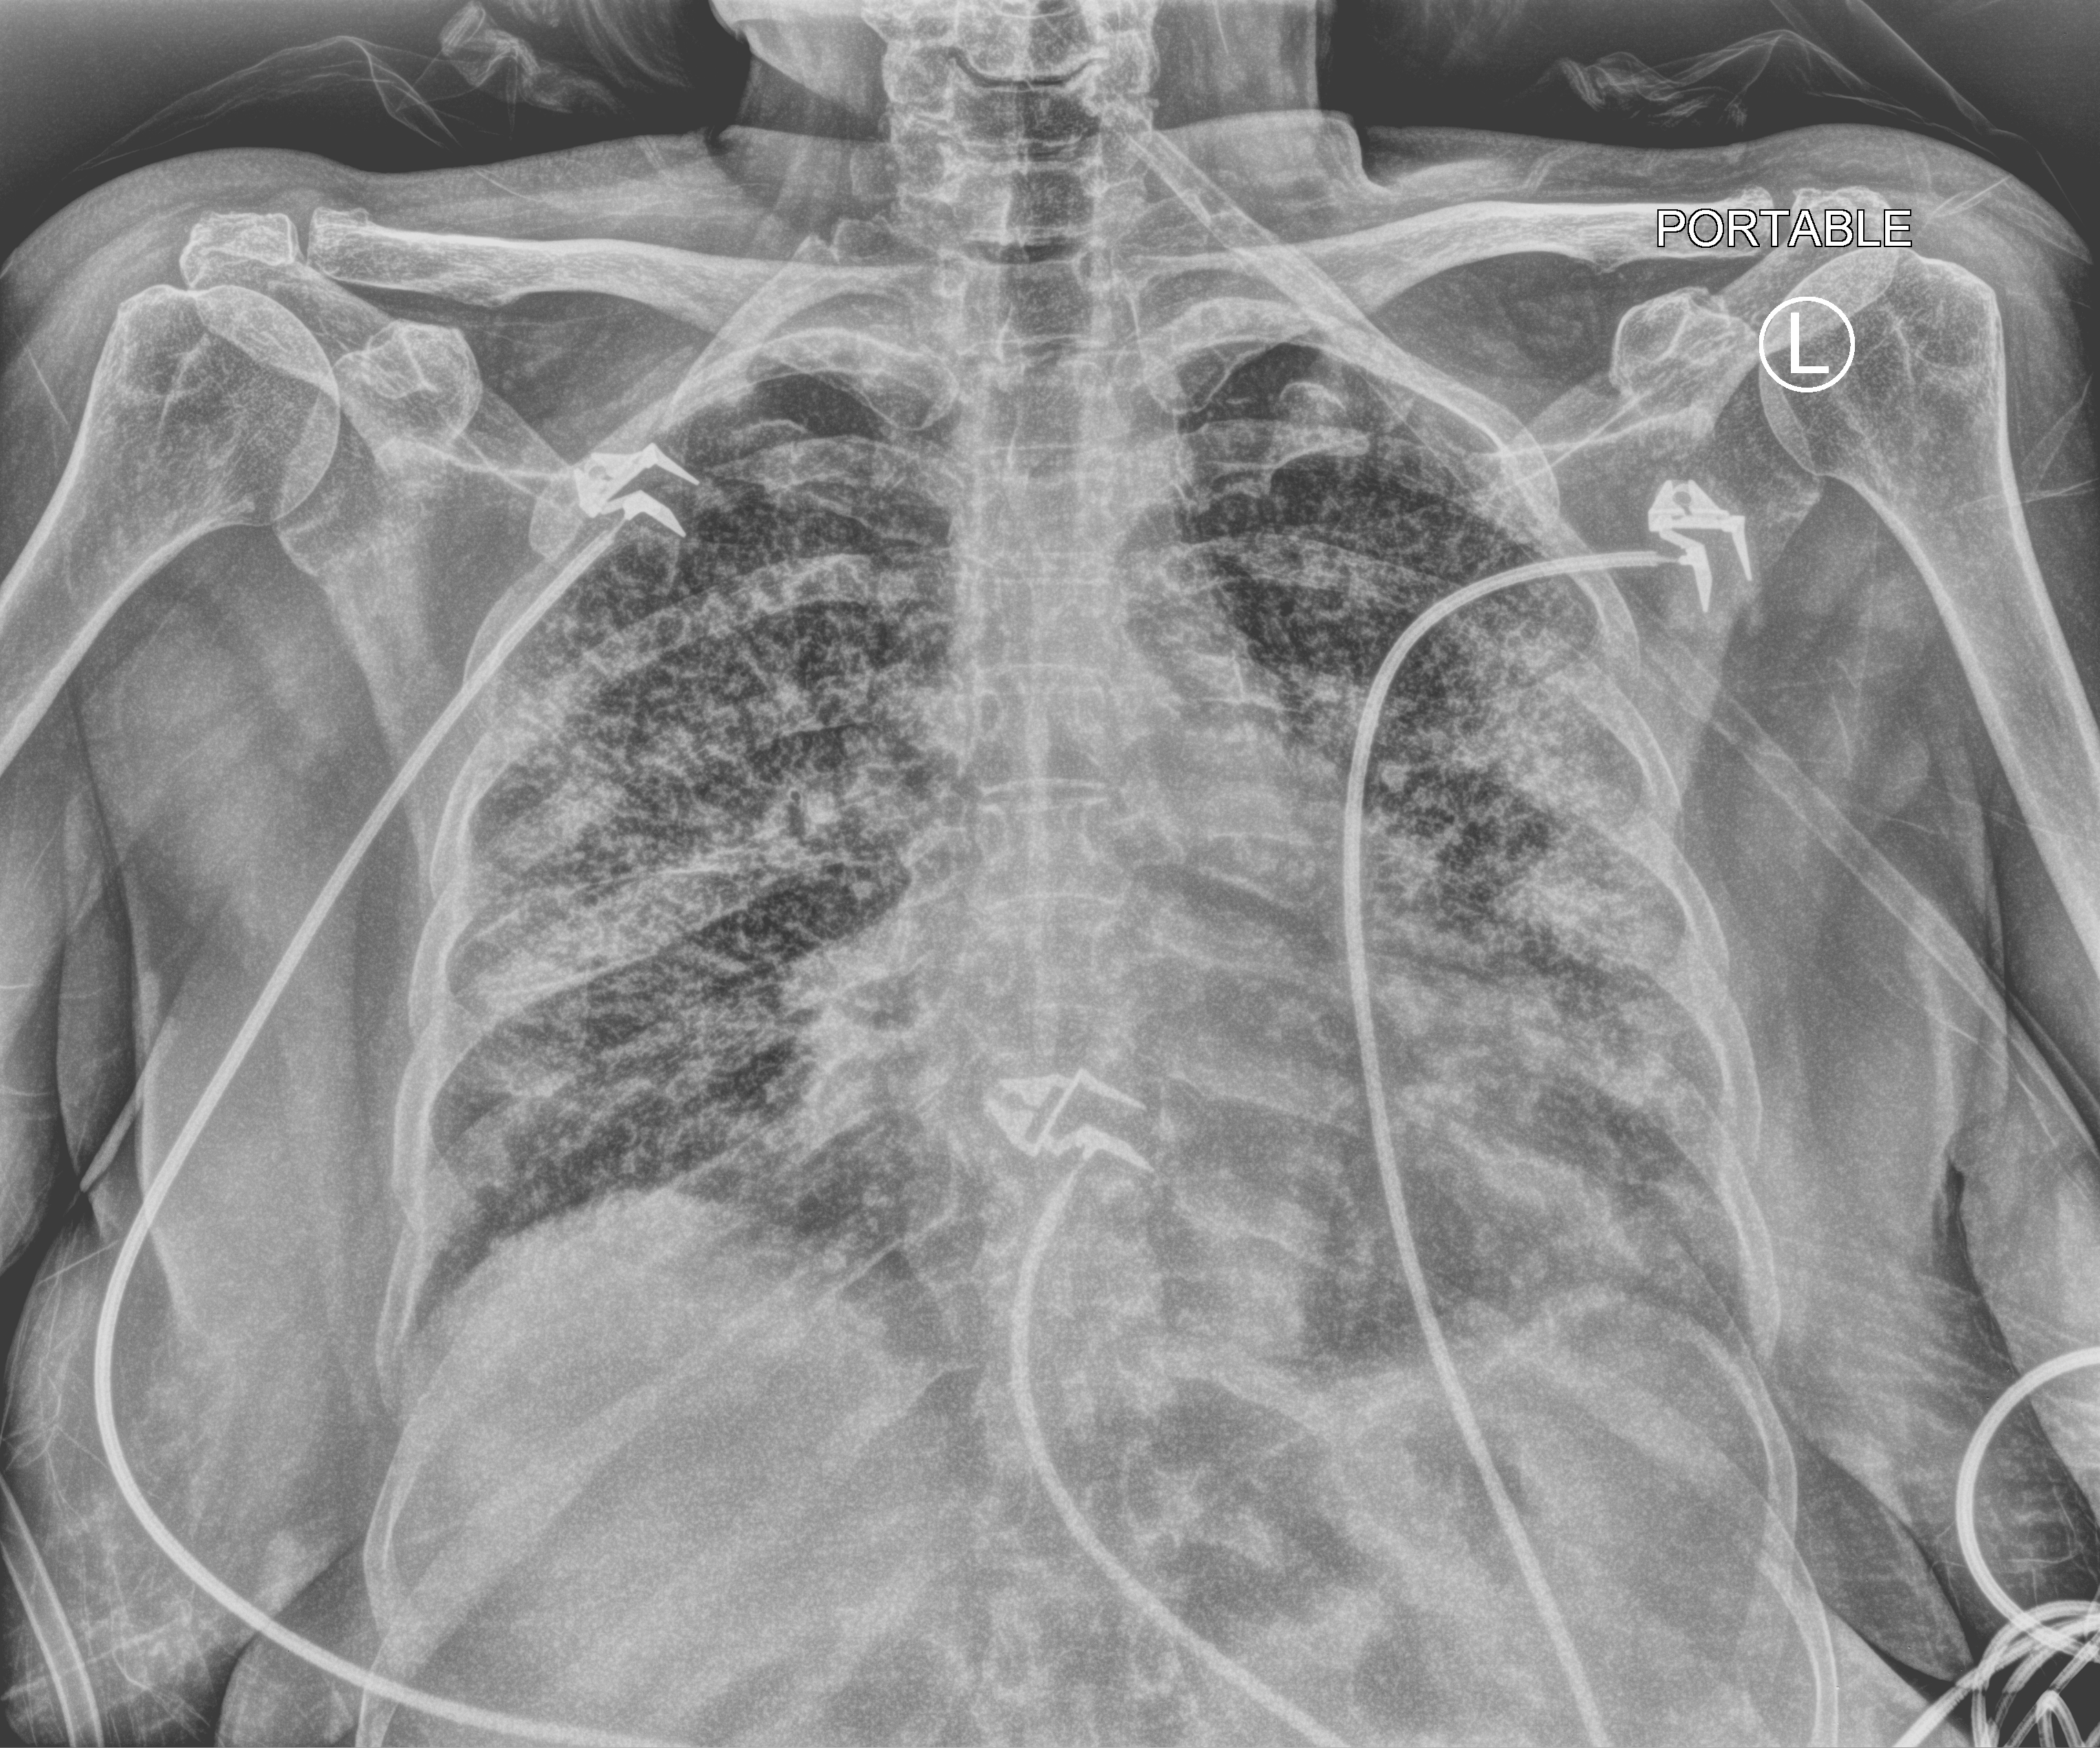
Bedside chest radiograph (computed radiography), anteroposterior (AP) projection. Female patient hospitalised with COVID-19, age 60–74 years.
From the hospital-stay record, not from the radiograph (when in the stay this image was taken is not recorded): mechanically ventilated during this hospital stay: yes; length of hospital stay: 15 days.